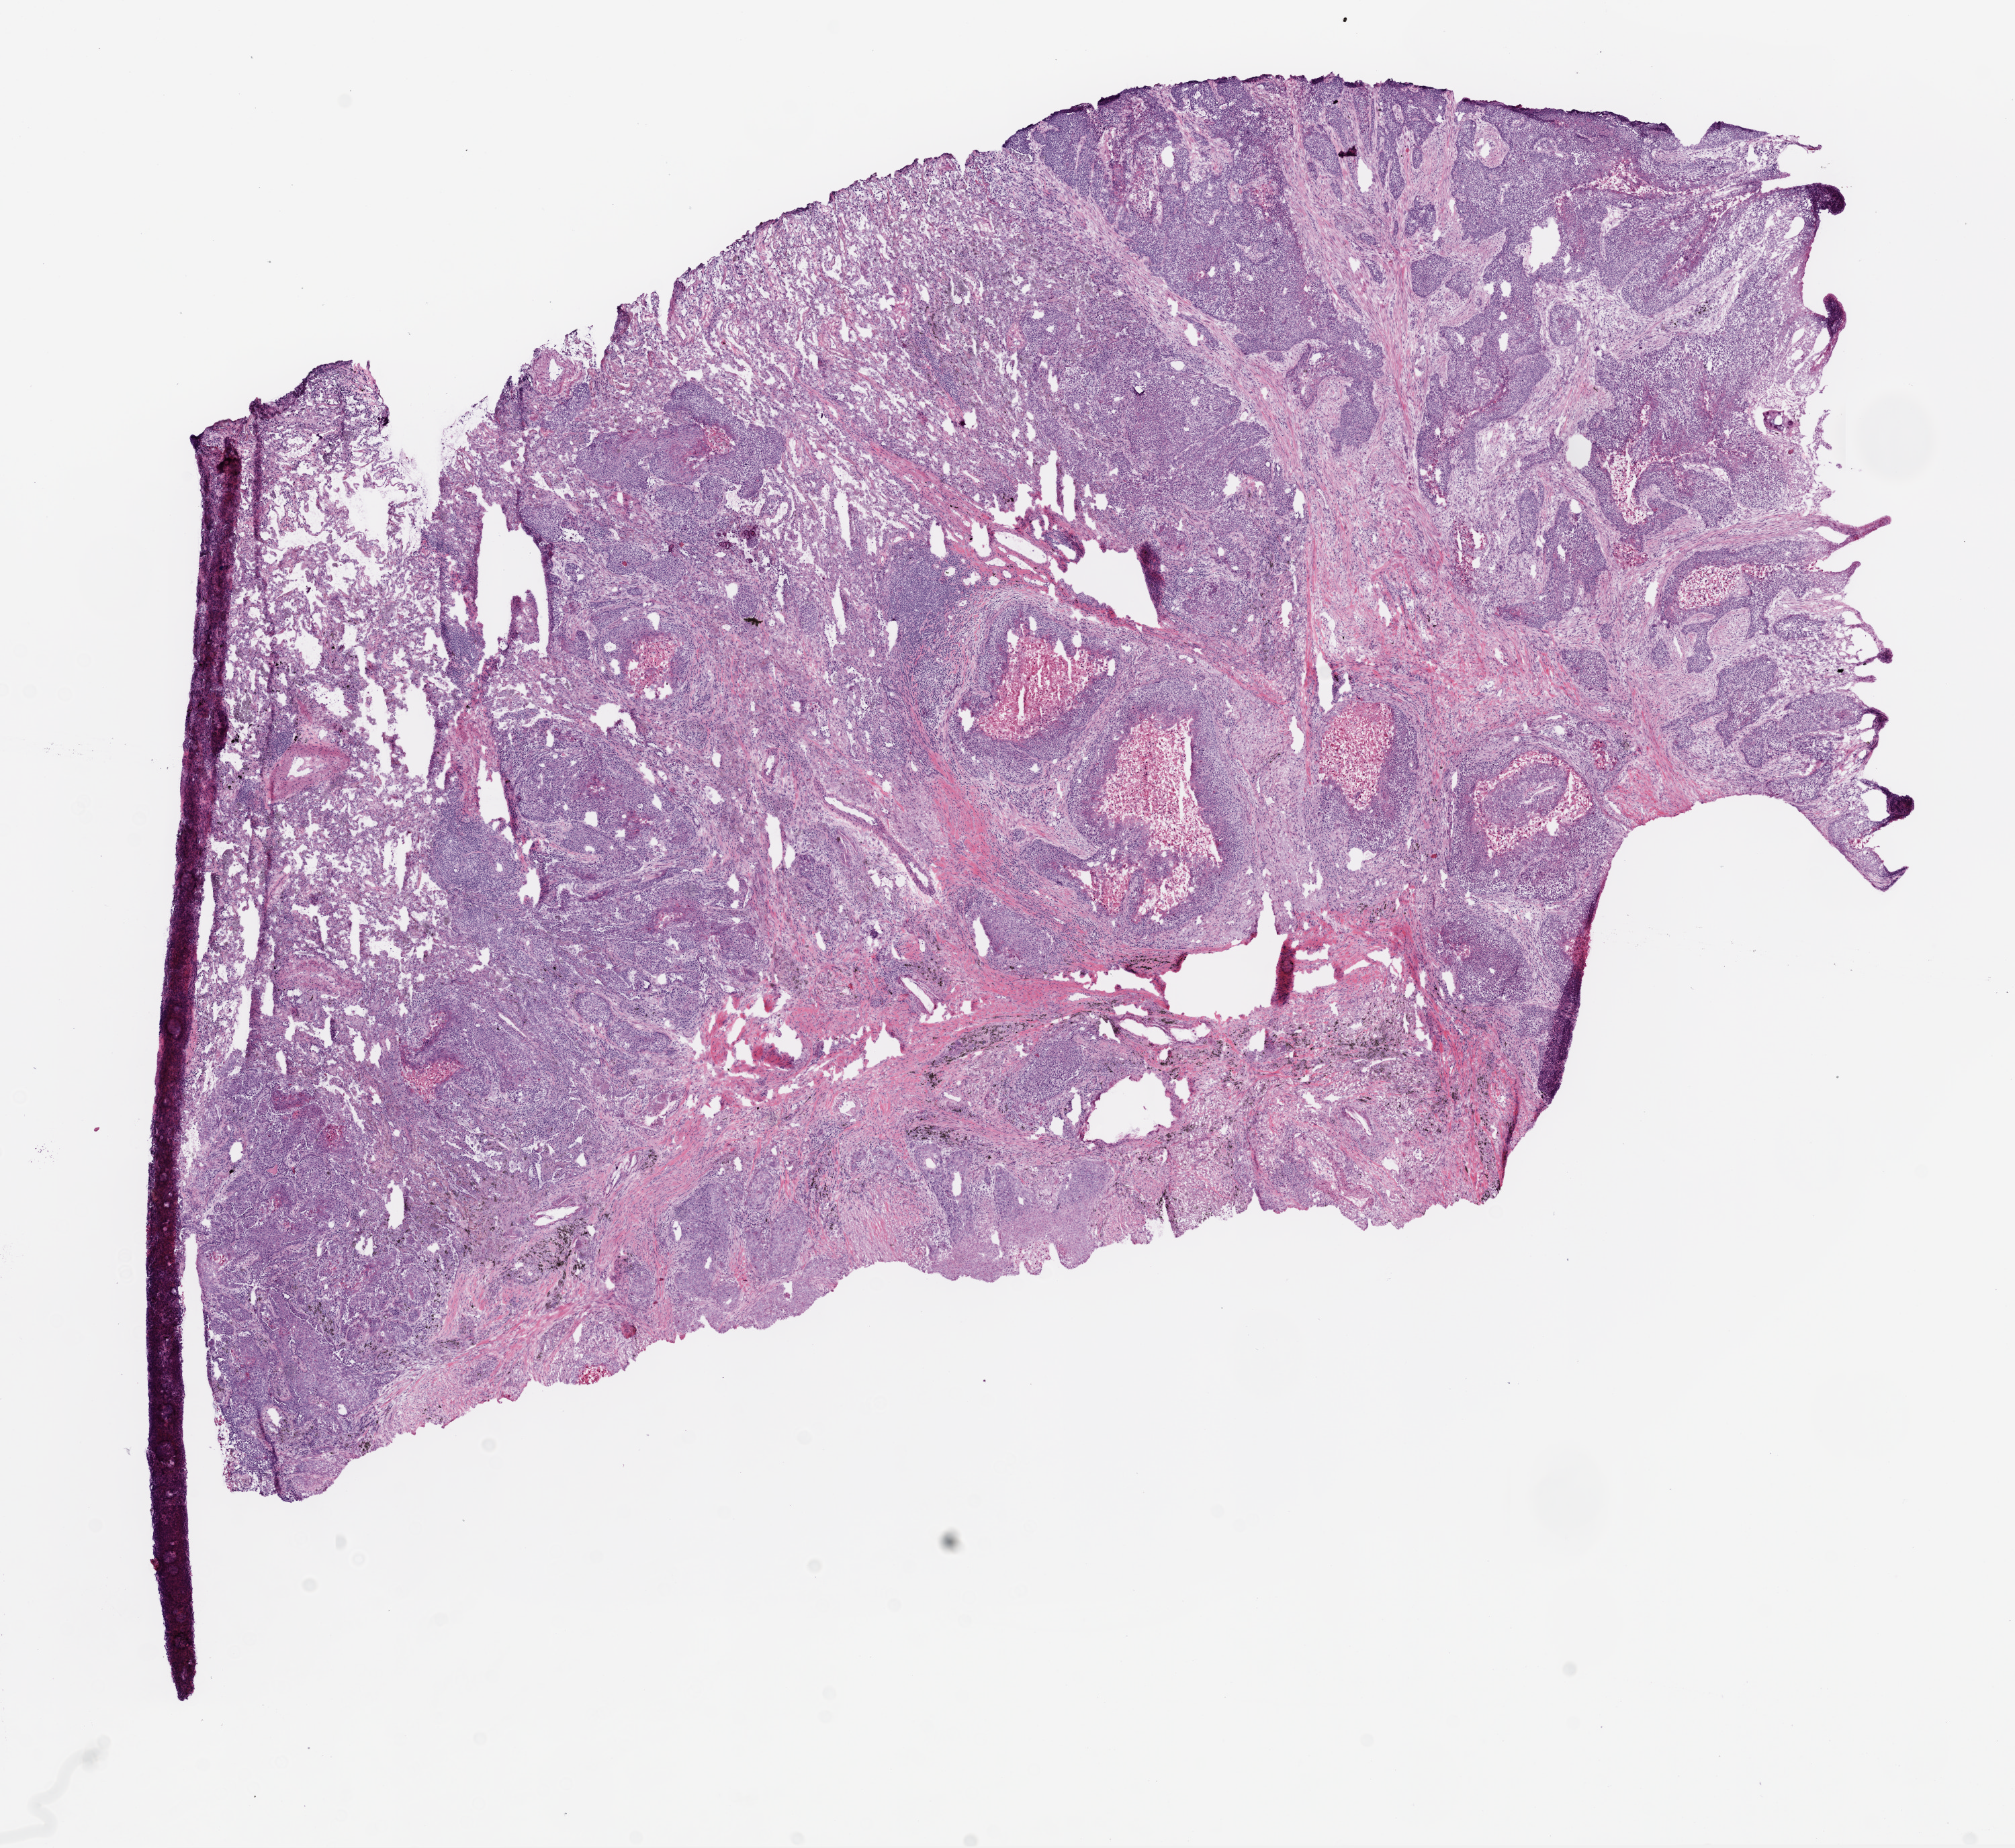
Digitized H&E tissue section (whole slide) — whole scanned area (about 12.0 x 11.0 mm) shown as a low-resolution overview. Frozen section from the bottom of the tissue portion. Primary tumour sample from the lung. Female patient; age at initial diagnosis 67 years. Pathologist review of this section (percent, as recorded): tumour cells 76%, tumour nuclei 90%, normal cells 7%, stromal cells 10%, necrosis 7%.
• AJCC pathologic stage: IIA (6th edition)
• diagnosis: Squamous cell carcinoma, NOS
• TNM: T1 N1 M0
• laterality: left